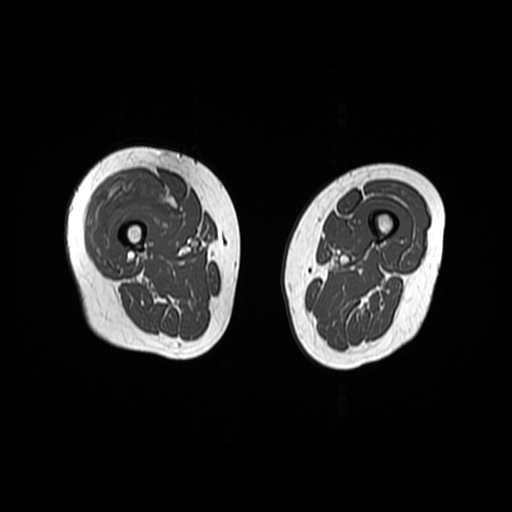
MRI of an extremity soft-tissue mass, one axial slice. Position 18 of 48 along the scan axis. 6 mm slice thickness. 512 × 512 image matrix. Female patient. Case-level facts recorded for this patient, not image findings: histological type: pleiomorphic undifferentiated sarcoma; grade: high; site of the primary tumour: right quadricep.
Structures marked on this image (manually delineated by an expert):
- gross tumour volume including surrounding oedema: bounding box (x1, y1, x2, y2) in pixels: (89, 175, 176, 261)